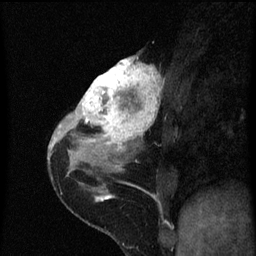
Breast MRI (dynamic contrast-enhanced), one sagittal slice. Dynamic contrast-enhanced series, image 2 of 3 at this slice position (ordered by acquisition). 1.5 T. TE 4.2 ms, TR 8 ms. 256 × 256 image matrix, field of view 180 × 180 mm. Patient: female, 38 years.
Structures marked on this image (semi-automatic segmentation, software-assisted and operator-edited):
- analysis volume of interest (the breast-tissue region the enhancement analysis was run in; not a lesion): box from (x=80, y=54) to (x=163, y=151) px
- tumour enhancement mask (voxels above the 70 % enhancement threshold inside the analysis volume of interest): (x=80, y=58)–(x=161, y=151)